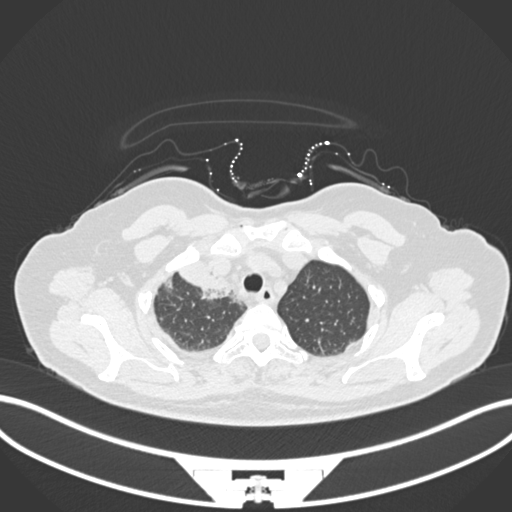
Chest CT, one axial slice; position 143 of 172 along the scan axis; 120 kVp; lung window (W 1500 / L -600 HU); 1 mm slice thickness; 512 × 512 image matrix, field of view 400 × 400 mm. Female patient, age 52 years. From the clinical record (not read from this slice): clinical TNM (as recorded): T3 N1 M1.
Structures marked on this image (bounding box drawn by a radiologist):
- lung tumour (recorded histology: adenocarcinoma): bounding box (x1, y1, x2, y2) in pixels: (171, 262, 236, 306)